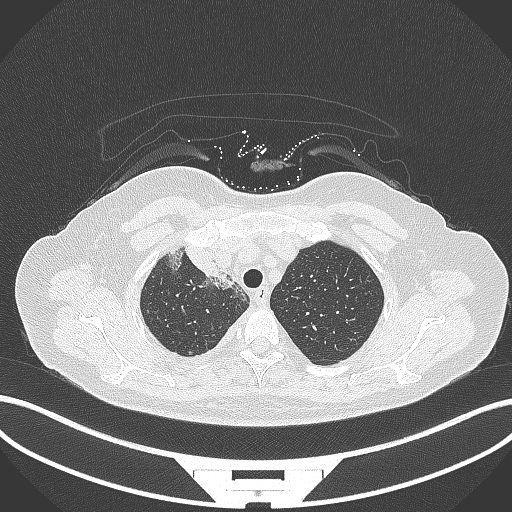
Chest CT, one axial slice; position 256 of 305 along the scan axis; reconstruction kernel B70f; lung window (W 1500 / L -600 HU); 1 mm slice thickness; 512 × 512 image matrix. Female patient, age 52 years. Case-level facts recorded for this patient, not image findings: clinical TNM (as recorded): T3 N1 M1.
Outlined on this slice (rectangle marked by the reading radiologist):
- lung tumour (recorded histology: adenocarcinoma): bounding box <181,242,222,281> (left, top, right, bottom; pixels)